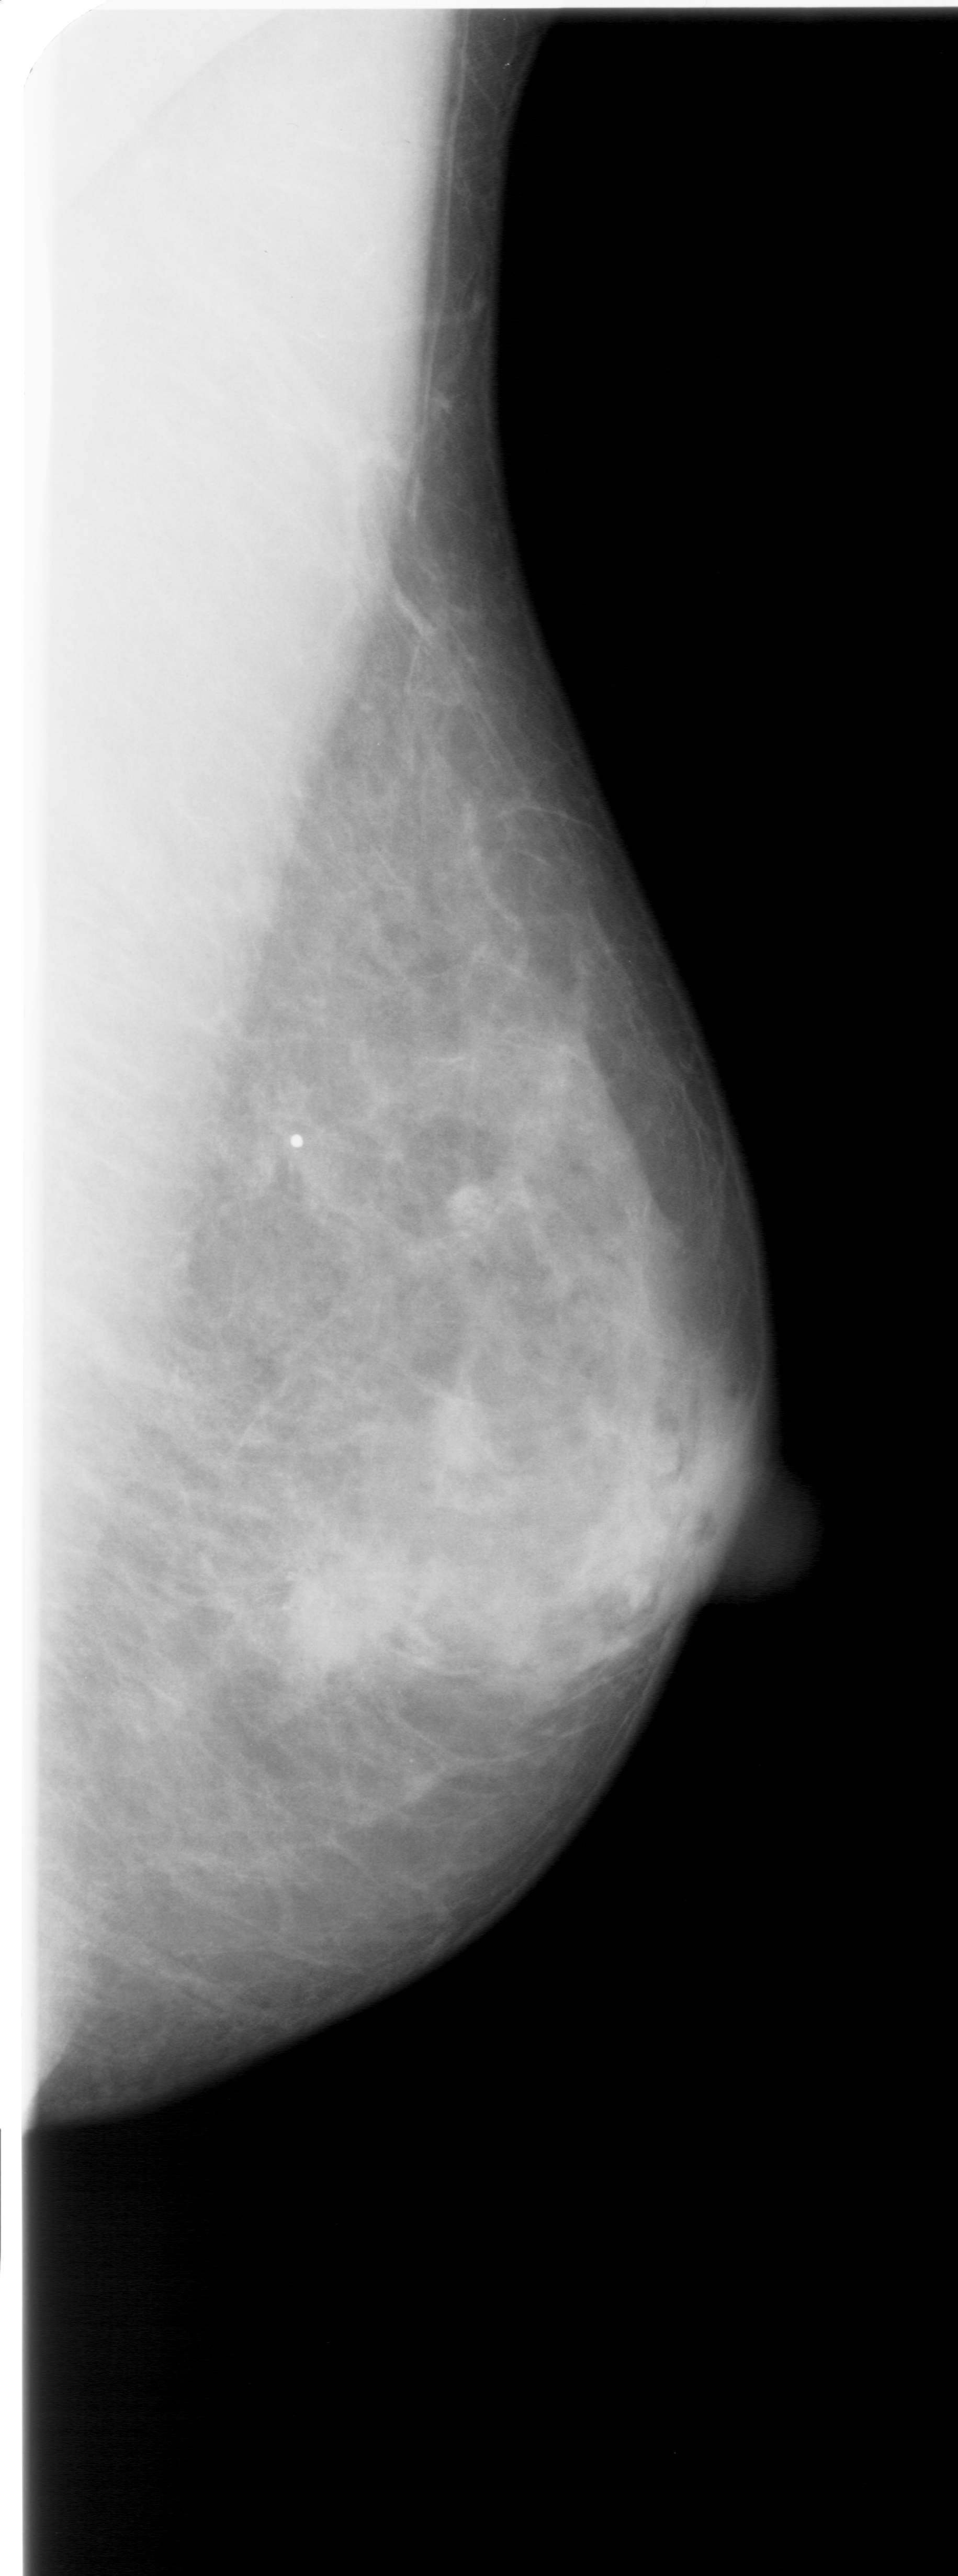
Digitized screen-film mammogram. Right breast. Mediolateral oblique (MLO) view. BI-RADS breast density category 4 (scale 1–4). 958 × 2576 image matrix.
Expert-marked regions of interest on this image (one box per marked abnormality):
- calcifications, morphology pleomorphic, distribution clustered; BI-RADS assessment category 5; pathology (as recorded): malignant: box from (x=152, y=1421) to (x=526, y=1787) px